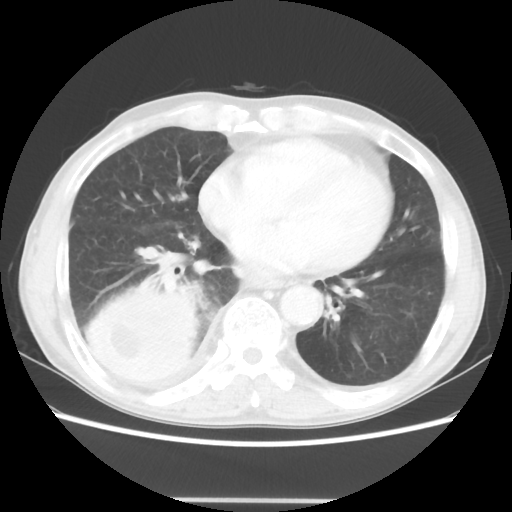
Chest CT, one axial slice. Position 16 of 48 along the scan axis. Lung window (W 1500 / L -600 HU). 5 mm slice thickness. 512 × 512 image matrix, field of view 361 × 361 mm. Patient: male, 66 years. Case-level facts recorded for this patient, not image findings: clinical TNM (as recorded): T4 N1 M1; histopathological grade: G3.
Outlined on this slice (rectangle marked by the reading radiologist):
- lung tumour (recorded histology: small cell carcinoma): bounding box <79,272,203,400> (left, top, right, bottom; pixels)